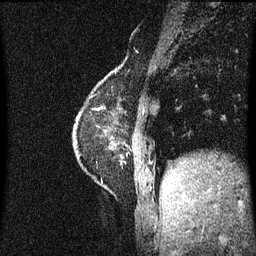
Breast MRI (dynamic contrast-enhanced), one sagittal slice. Position 14 of 60 along the scan axis. Dynamic contrast-enhanced series, image 2 of 3 at this slice position (ordered by acquisition). 1.5 T. TE 4.2 ms, TR 8.4 ms. 2 mm slice thickness. 256 × 256 image matrix, field of view 200 × 200 mm. Patient: female, 60 years.
Structures marked on this image (semi-automatic segmentation, software-assisted and operator-edited):
- analysis volume of interest (the breast-tissue region the enhancement analysis was run in; not a lesion): bounding box (x1, y1, x2, y2) in pixels: (71, 72, 127, 193)
- tumour enhancement mask (voxels above the 70 % enhancement threshold inside the analysis volume of interest): (77, 82, 126, 147)